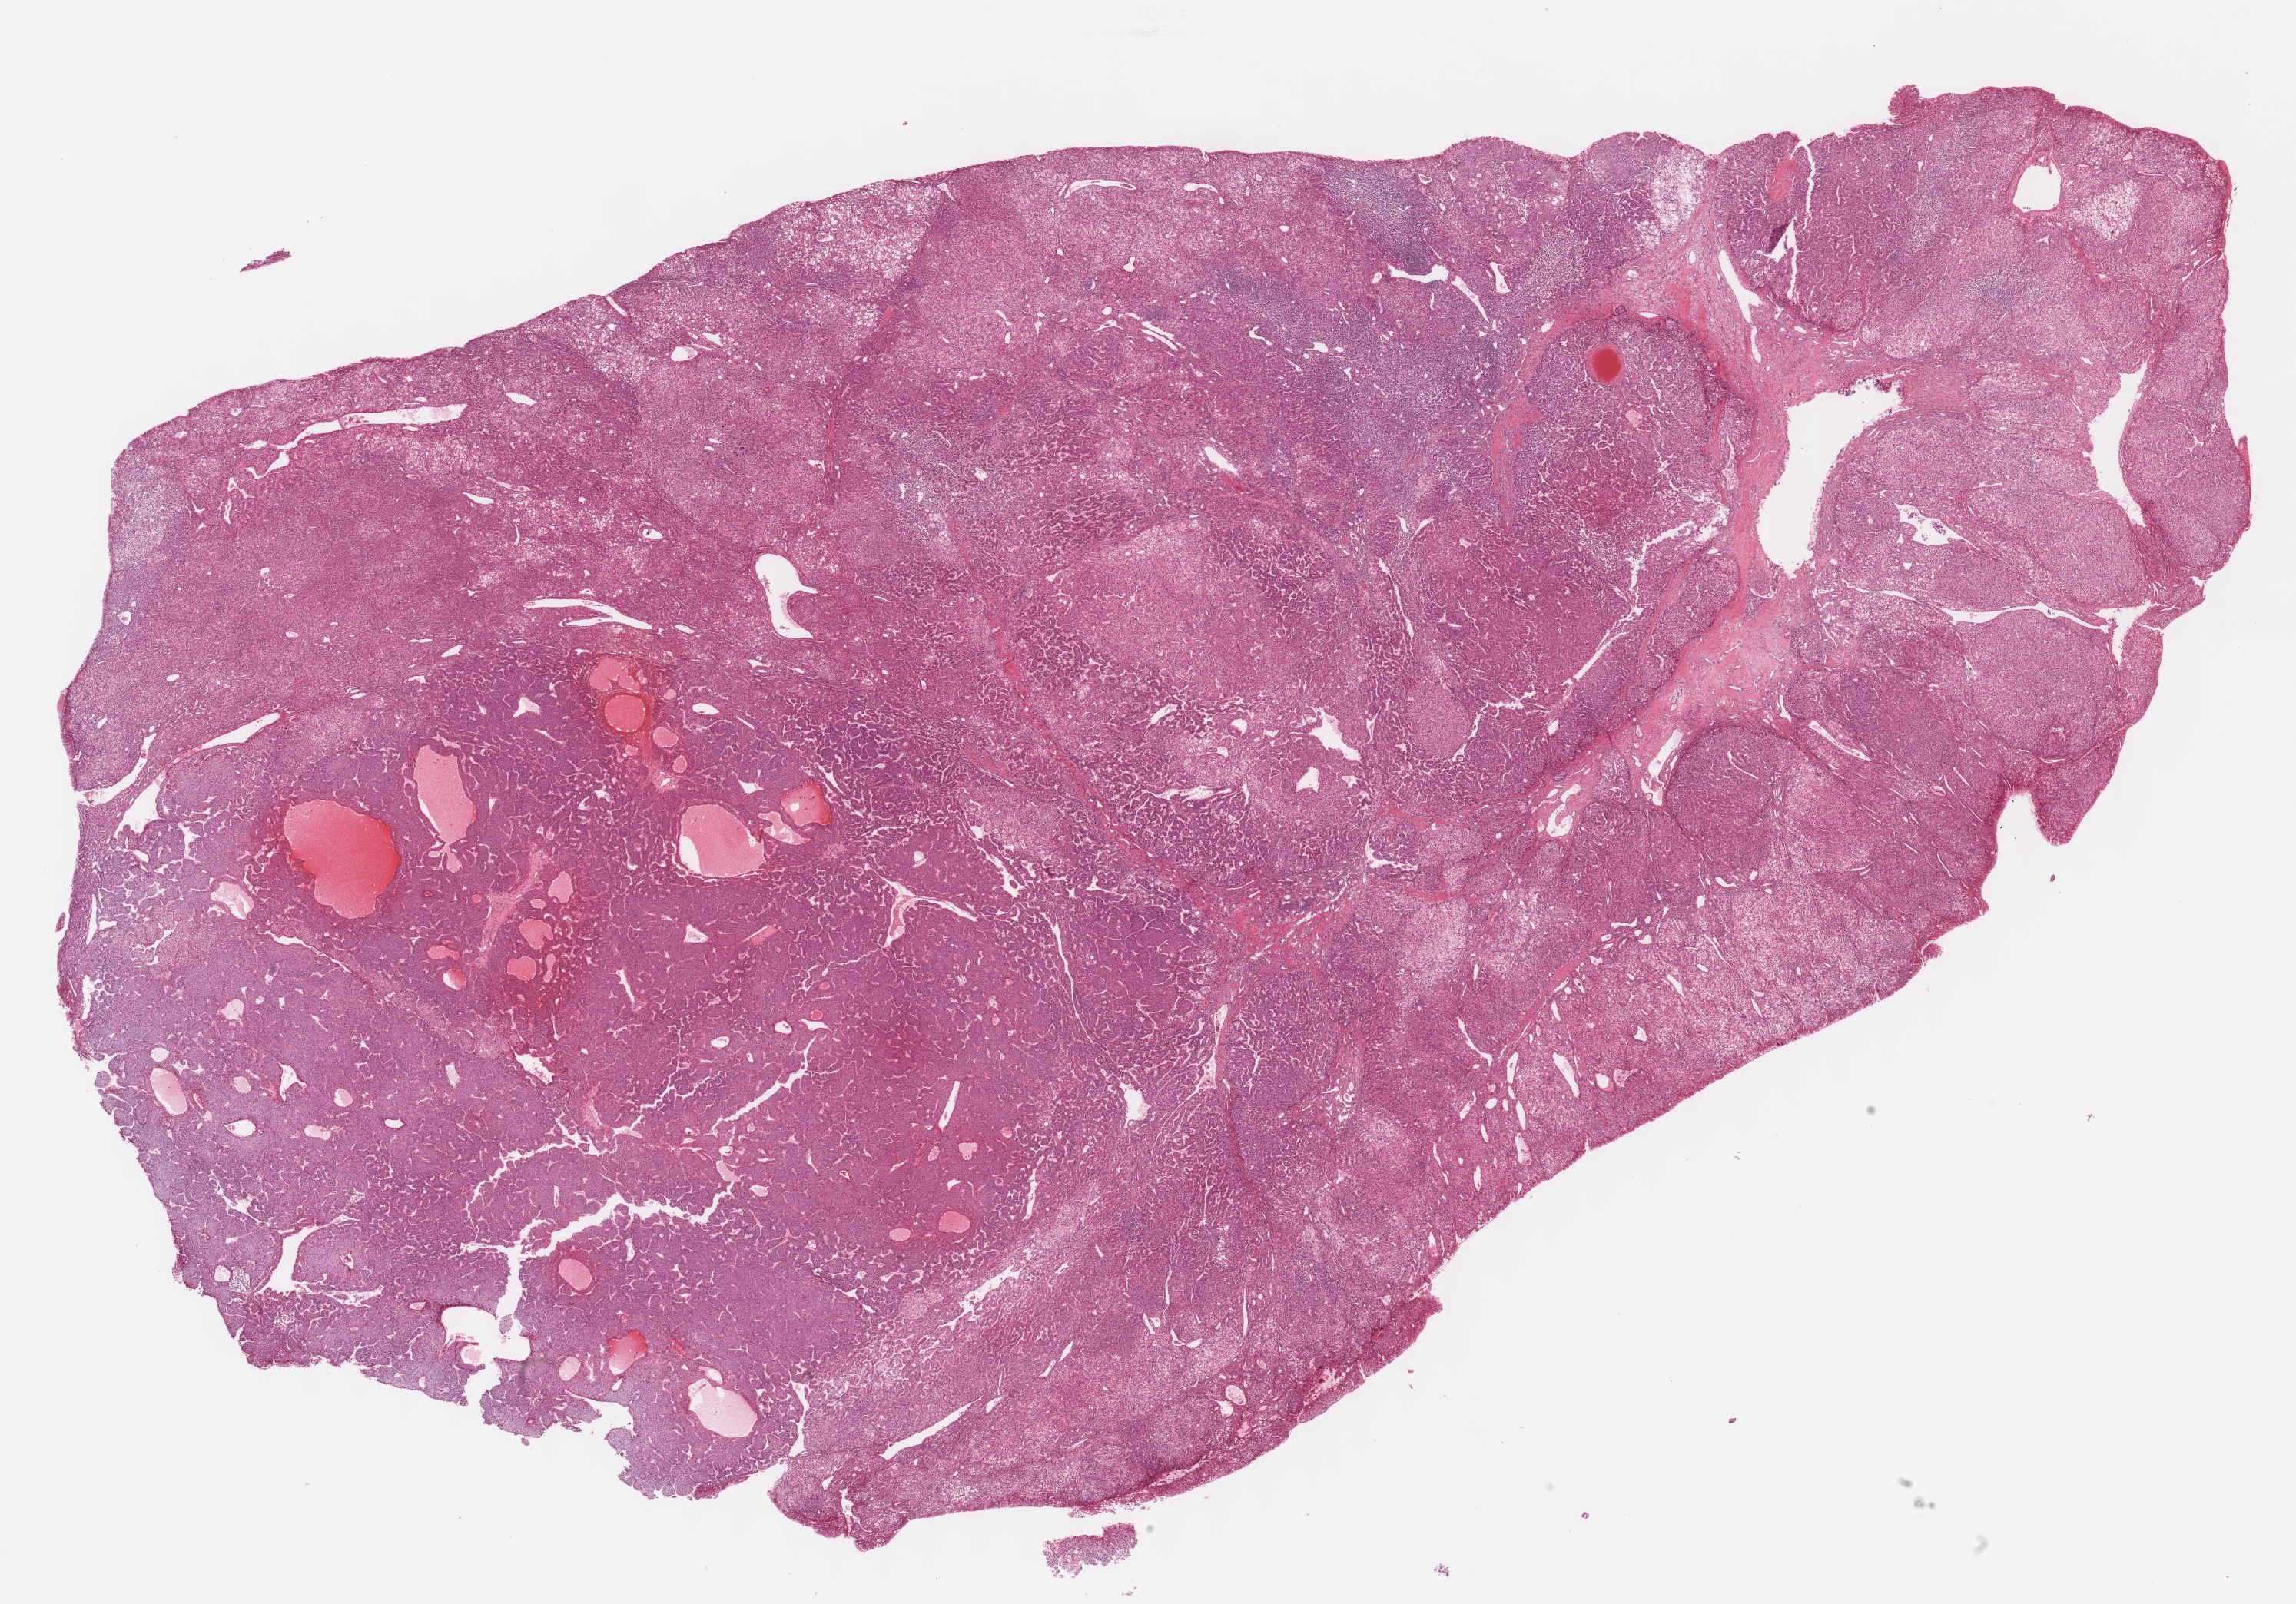
Digitized Hematoxylin and eosin (H&E) stained tissue section (whole slide), shown as a low-resolution overview of the whole scanned area (about 24.1 x 16.9 mm); formalin-fixed paraffin-embedded (FFPE) diagnostic section; liver, primary tumour sample. Male, age 51 years at initial diagnosis. Histologic grade: G3 (poorly differentiated).
AJCC pathologic stage: I (7th edition). Diagnosis: Hepatocellular carcinoma, NOS.